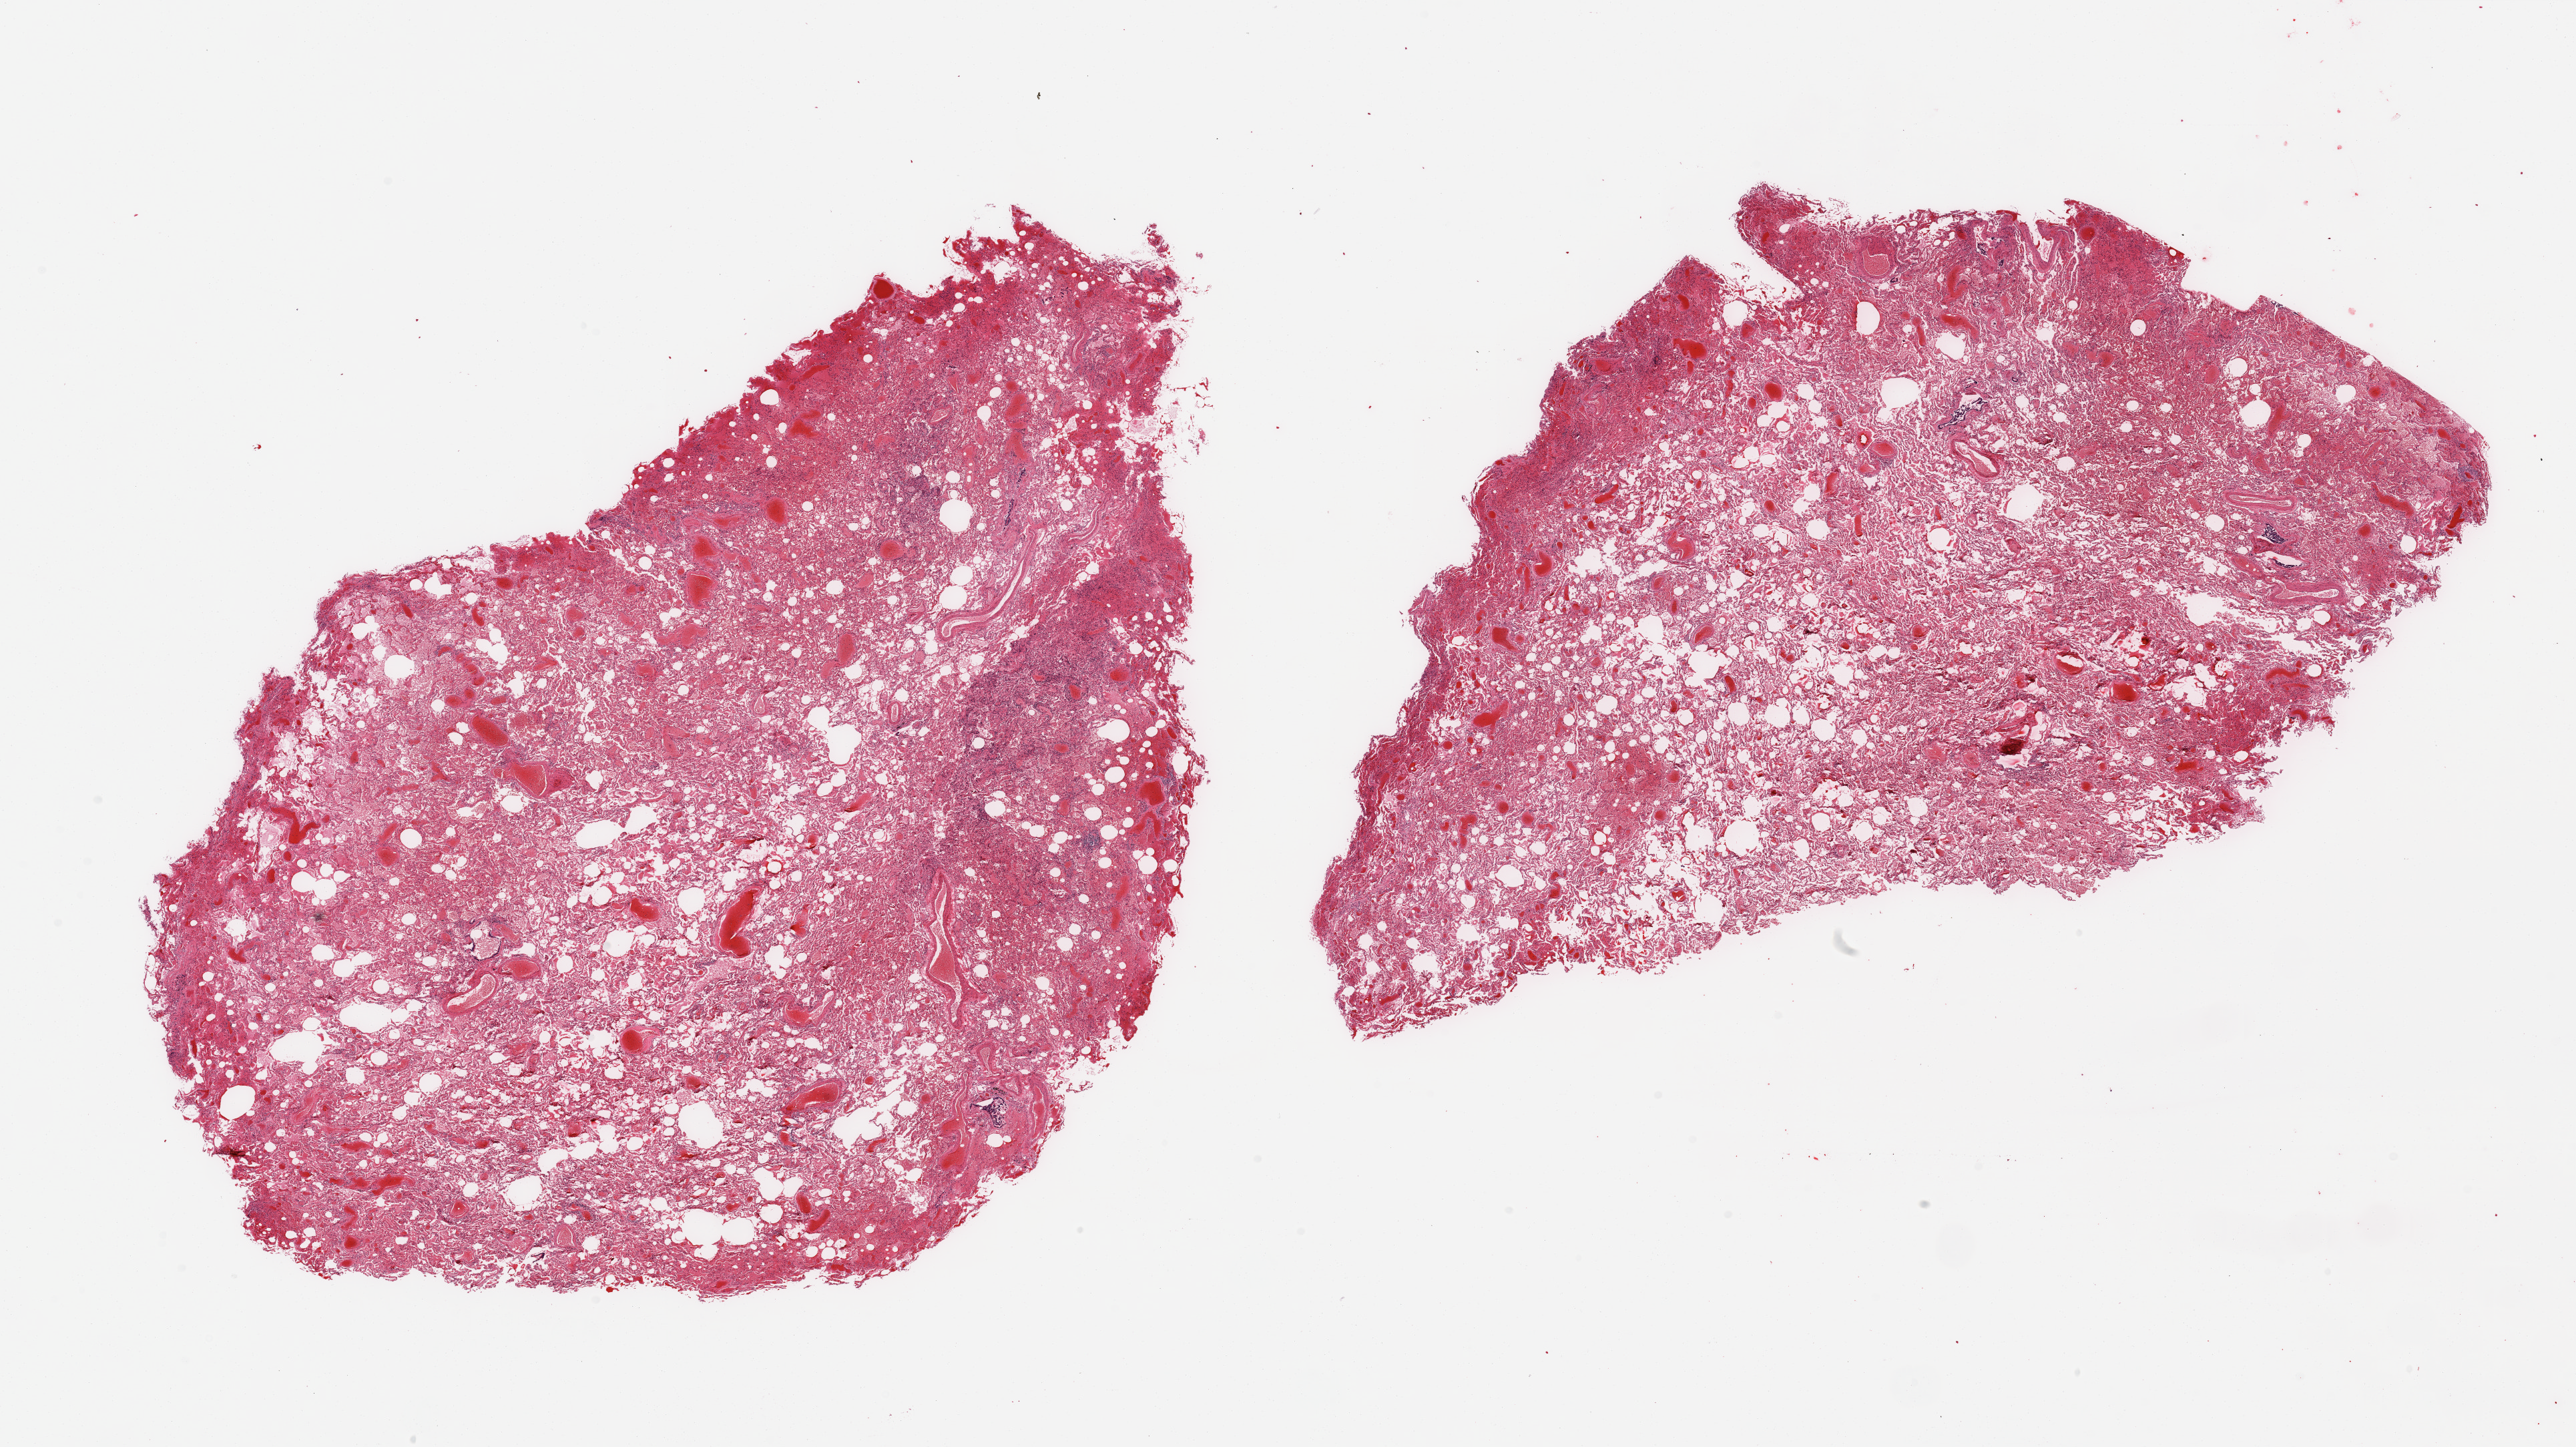
Digitized haematoxylin and eosin-stained section — shown as a low-resolution overview of the whole scanned area (about 30.5 x 17.1 mm, slide scanned at 20x). PAXgene-fixed, paraffin-embedded tissue. Section of lung (target tissue). Tissue donor sample.
Review note (as recorded): 2 pieces; congestion, hemorrhage, patchy inflammation.